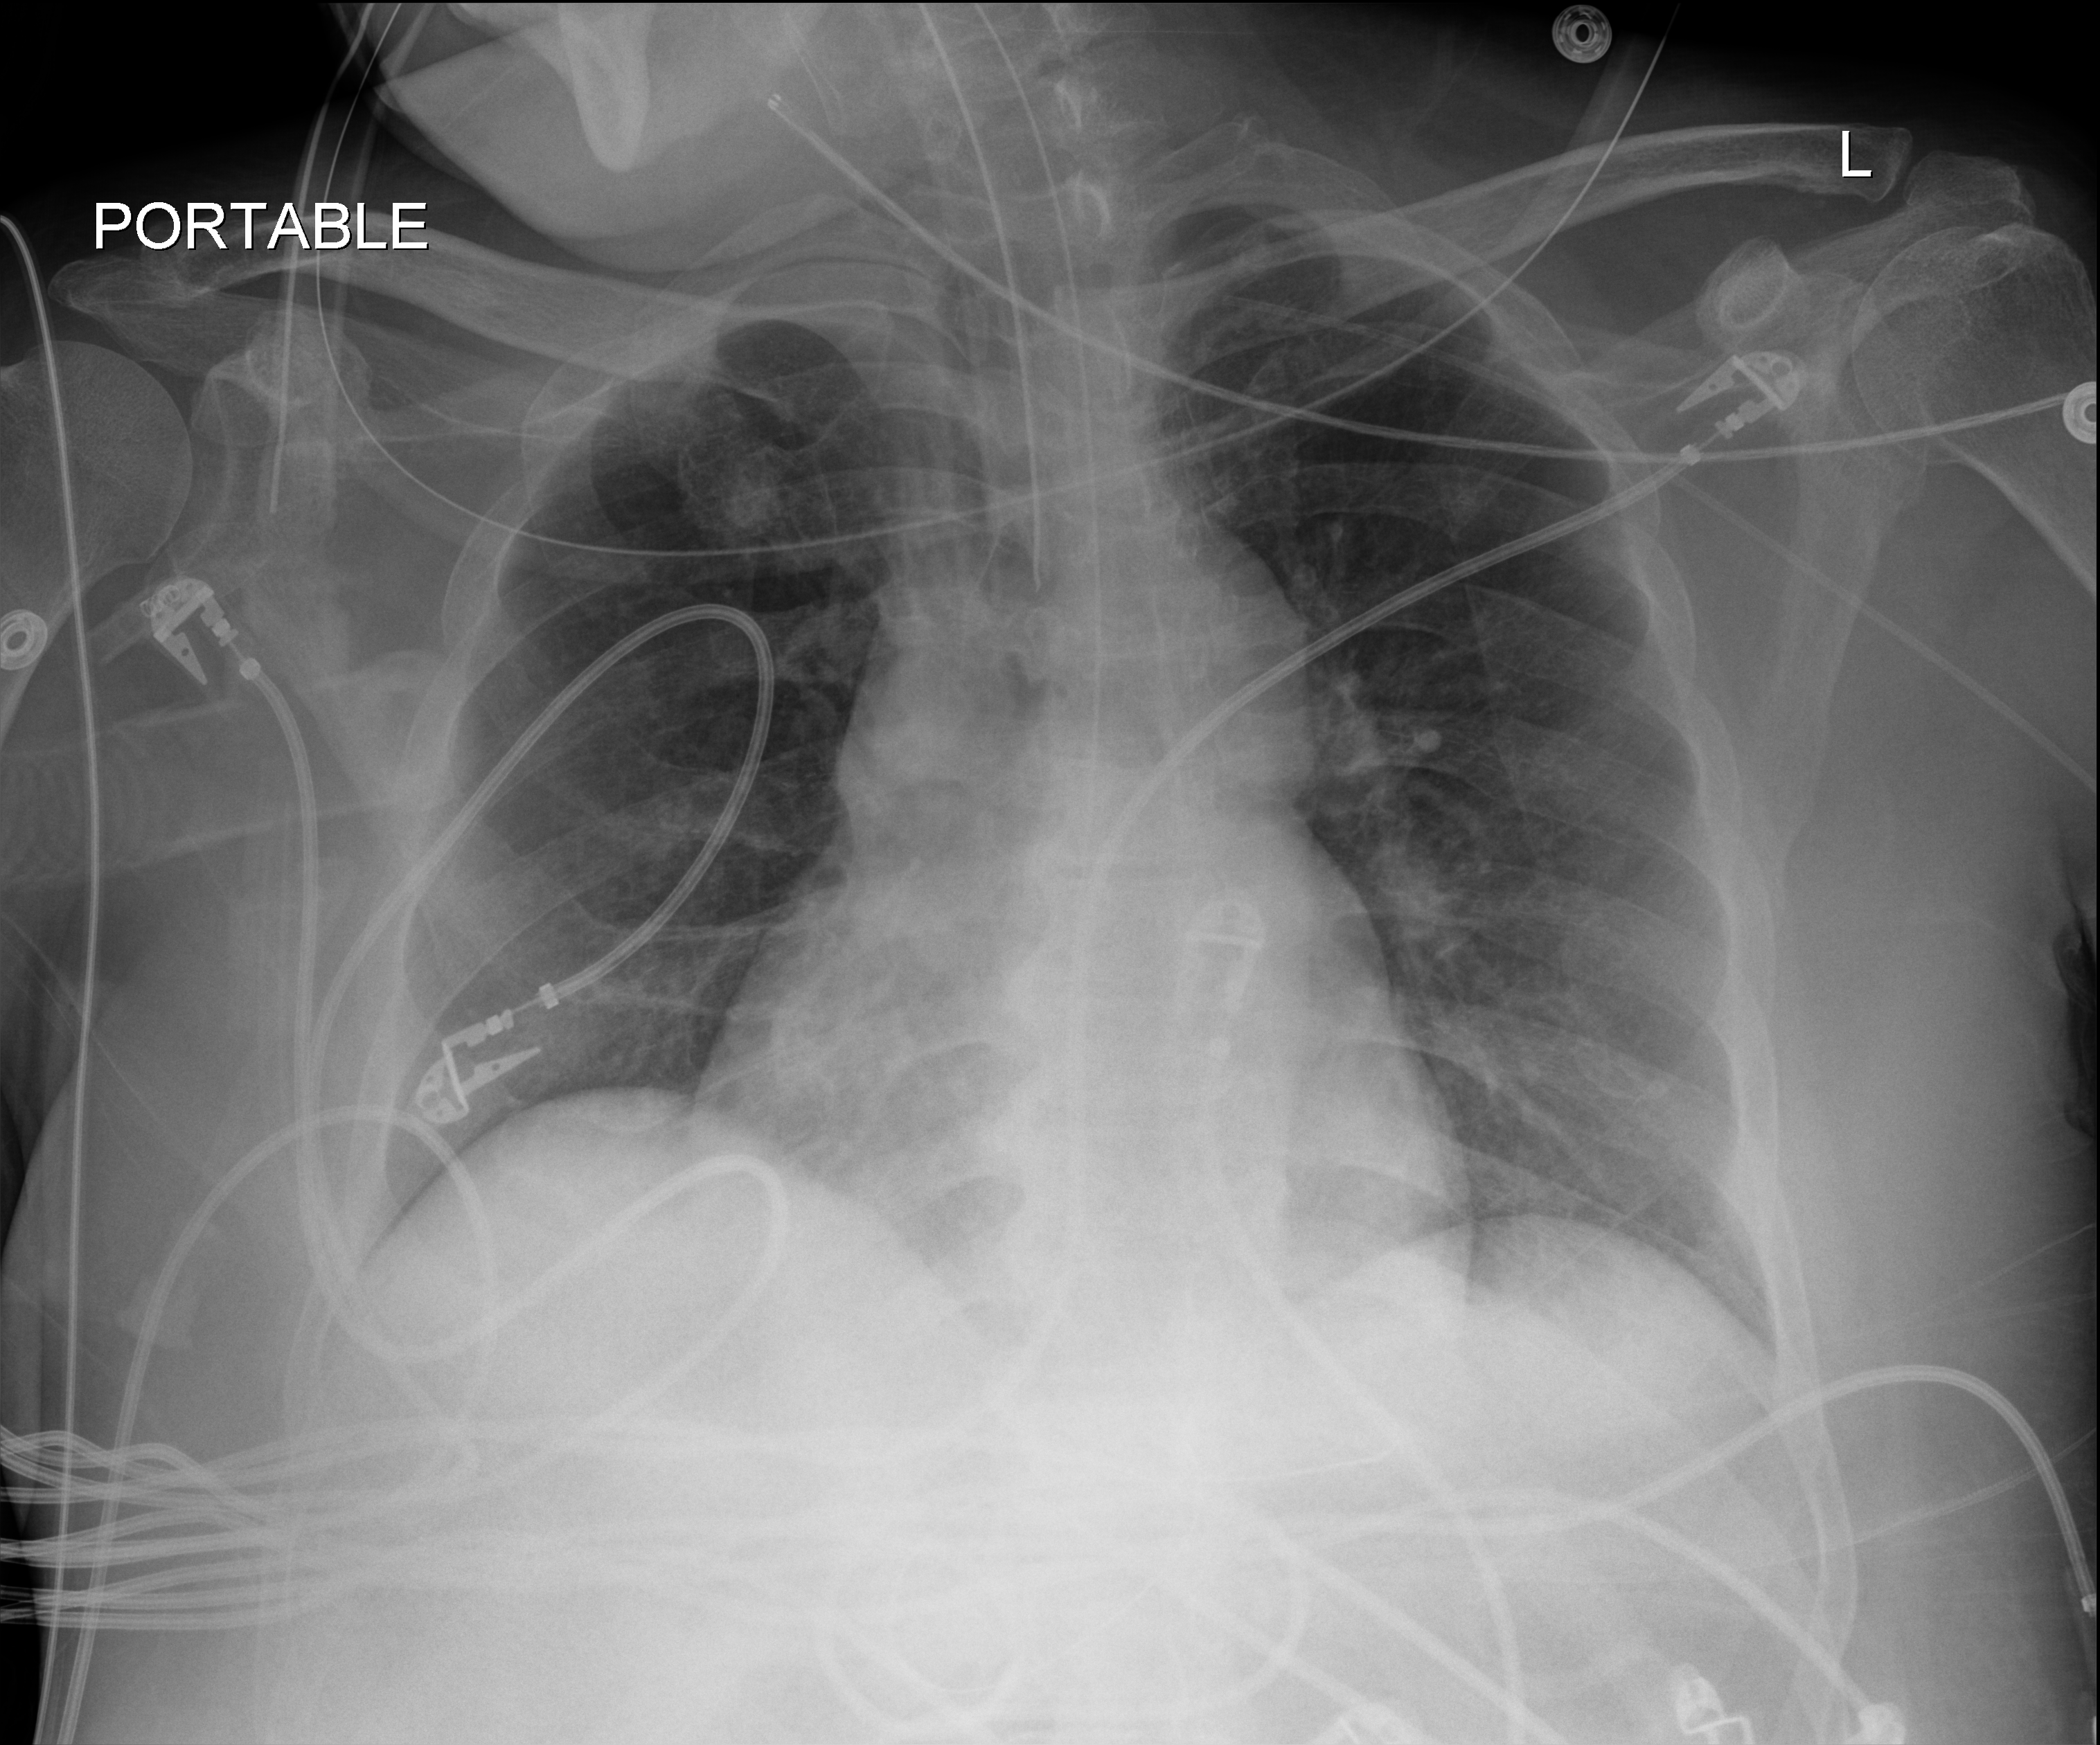
Bedside chest radiograph (digital radiography), anteroposterior (AP) projection. Patient hospitalised with COVID-19, aged 18–59 years.
From the hospital-stay record, not from the radiograph (when in the stay this image was taken is not recorded):
- length of hospital stay: 37 days